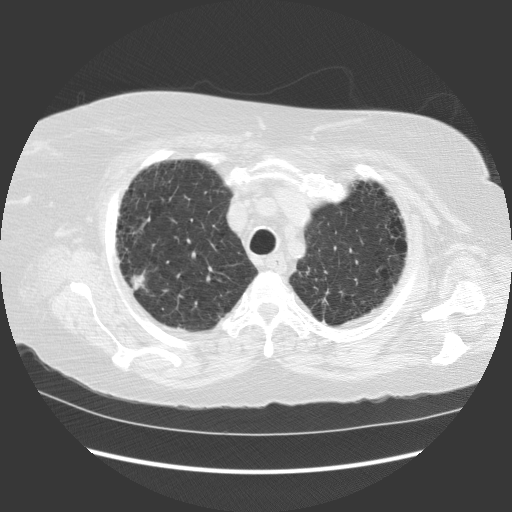
Axial slice from a low-dose chest CT screening exam; first (baseline) screen; lung window (W 1500 / L -600 HU); 2.5 mm slice thickness; 140 kVp; slice 99 of 121 in the series; 512 × 512 image matrix. Female, age 64 years at enrolment. Current smoker at enrolment.
Expert-annotated lung lesion, bounding box [x1, y1, x2, y2] px = [112, 260, 160, 303]. The screening reader recorded 2 non-calcified nodules or masses ≥4 mm on this exam (right upper lobe, left upper lobe); which of them this box marks is not recorded. Official screen result: positive, change unspecified: nodule(s) >= 4 mm or enlarging nodule(s), mass(es), or other non-specific abnormalities suspicious for lung cancer. Lung cancer was diagnosed 69 days after this screen: small cell carcinoma, NOS, right upper lobe, stage IV (AJCC 6th edition), 20 mm at pathology.